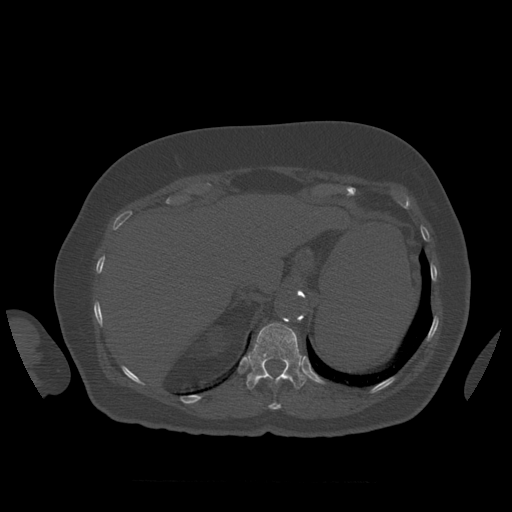
CT including the spine, one axial slice; position 306 of 399 along the scan axis; reconstruction kernel STANDARD; 120 kVp; bone window (W 1800 / L 400 HU); 512 × 512 image matrix. Patient age 81 years. From the clinical record (not read from this slice): primary cancer: renal; vertebrae with lytic lesions (as recorded): L1.
Structures marked on this image (semi-automatically segmented with operator editing):
- T11 vertebra: box from (x=269, y=402) to (x=282, y=410) px
- T12 vertebra: (x=246, y=323)–(x=307, y=390)